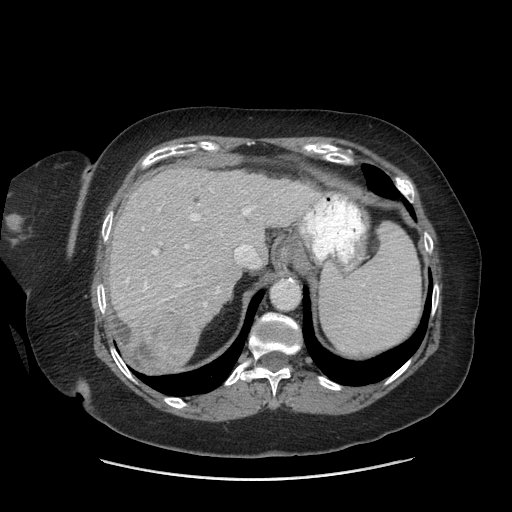
Contrast-enhanced abdominal CT (liver protocol), one axial slice. Slice 54 of 69 in the series (ordered by position). Reconstruction kernel STANDARD. Soft-tissue window (W 400 / L 40 HU). 2.5 mm slice thickness. 512 × 512 image matrix. Case-level facts recorded for this patient, not image findings: diagnosis: hepatocellular carcinoma (patient treated with transarterial chemoembolisation; whether this scan precedes or follows treatment is not stated here); TNM stage (as recorded): Stage-IIIB; Child-Pugh class: A; tumour differentiation: moderately differentiated; tumour nodularity: multinodular.
Structures marked on this image (semi-automatically segmented with operator editing):
- liver parenchyma outside the tumour (the mass and vessels are separate outlines, so this box may not span the whole liver): bounding box [x1, y1, x2, y2] px = [108, 168, 318, 358]
- mass: [127, 308, 197, 373]
- liver vessels: [125, 207, 257, 309]